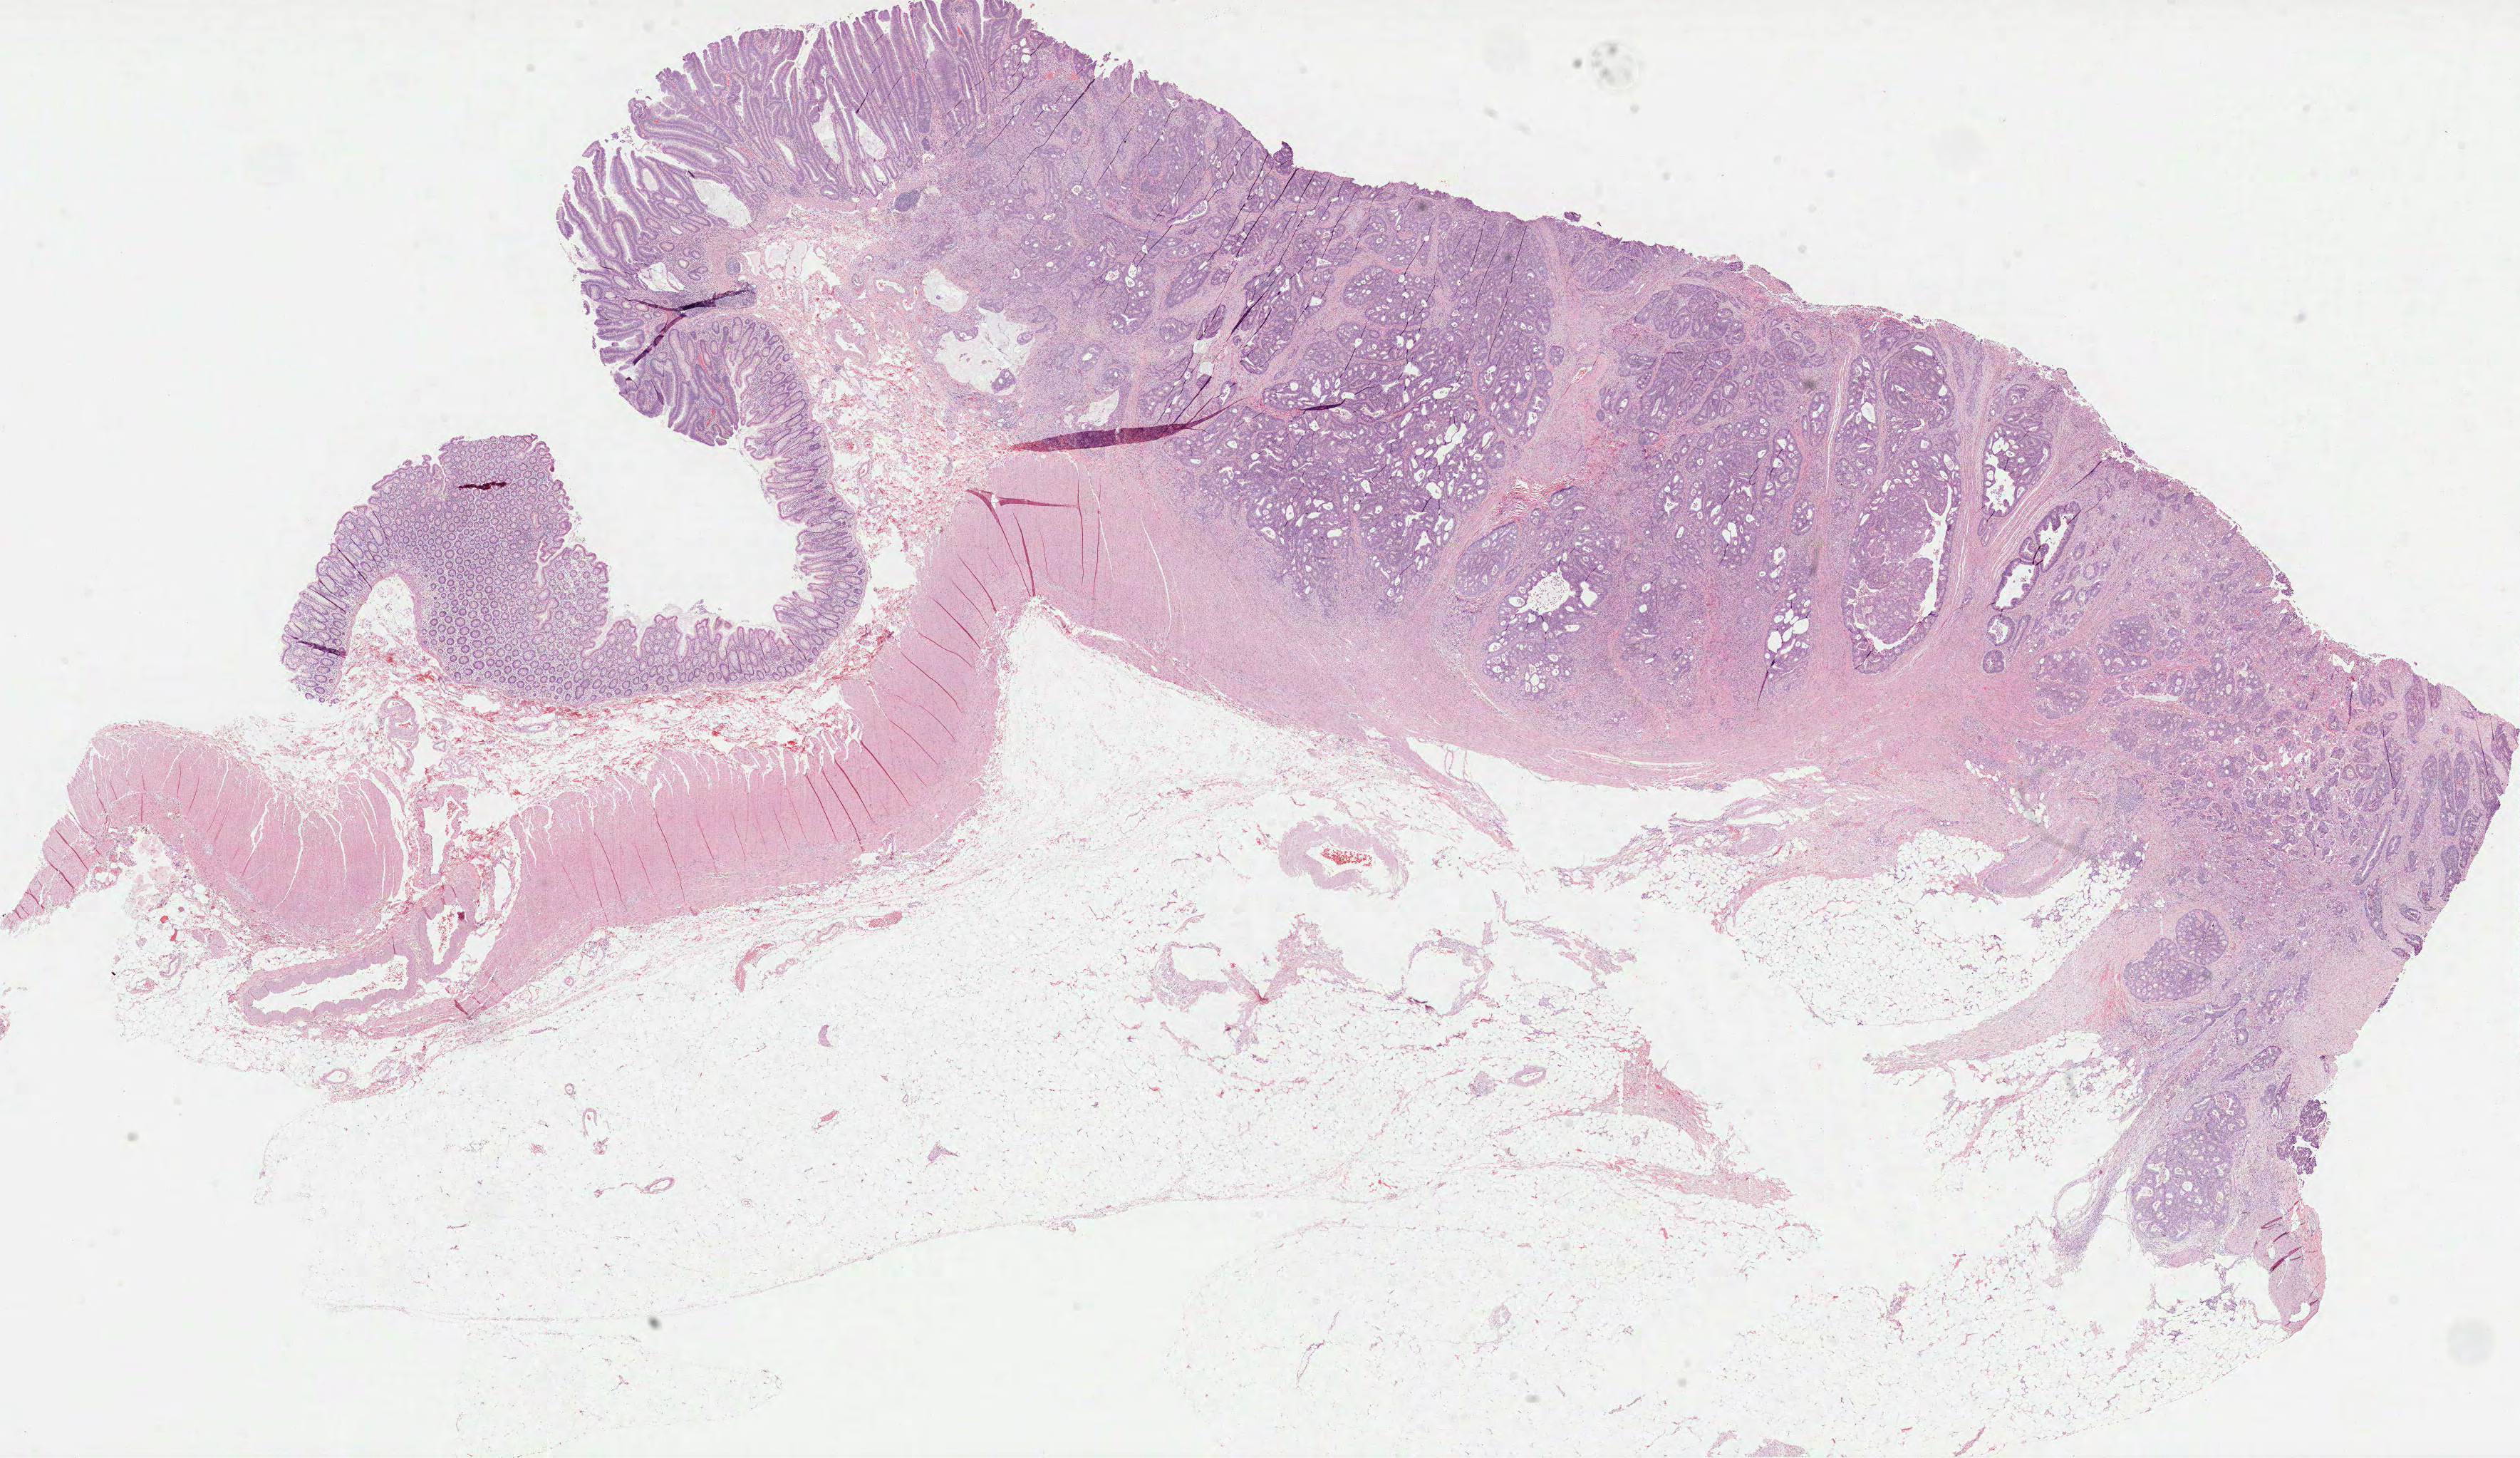
H&E-stained whole-slide image — a low-resolution overview of the entire scanned area, about 28.5 x 16.5 mm (acquisition: 40x scan). Formalin-fixed paraffin-embedded (FFPE) diagnostic section. Sample: primary tumour, colon. Male, age 73 years at initial diagnosis.
AJCC pathologic stage: III (6th edition). Lymph nodes positive (case pathology): 2 of 65 examined. Pathologic diagnosis: Adenocarcinoma, NOS (hepatic flexure of colon).